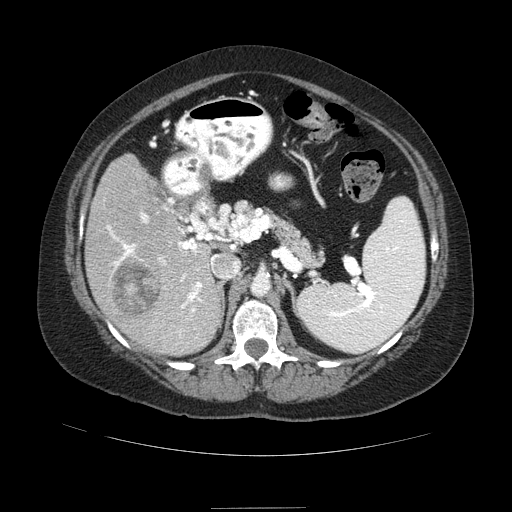
Contrast-enhanced abdominal CT (liver protocol), one axial slice; position 46 of 89 along the scan axis; reconstruction kernel STANDARD; soft-tissue window (W 400 / L 40 HU); 512 × 512 image matrix, field of view 400 × 400 mm. Case-level facts recorded for this patient, not image findings: diagnosis: hepatocellular carcinoma (patient treated with transarterial chemoembolisation; whether this scan precedes or follows treatment is not stated here); TNM stage (as recorded): Stage-IIIB; Child-Pugh class: A.
Structures marked on this image (semi-automatically segmented with operator editing):
- liver parenchyma outside the tumour (the mass and vessels are separate outlines, so this box may not span the whole liver): bounding box <86,154,222,356> (left, top, right, bottom; pixels)
- mass: <111,255,161,315>
- liver vessels: <106,198,219,339>